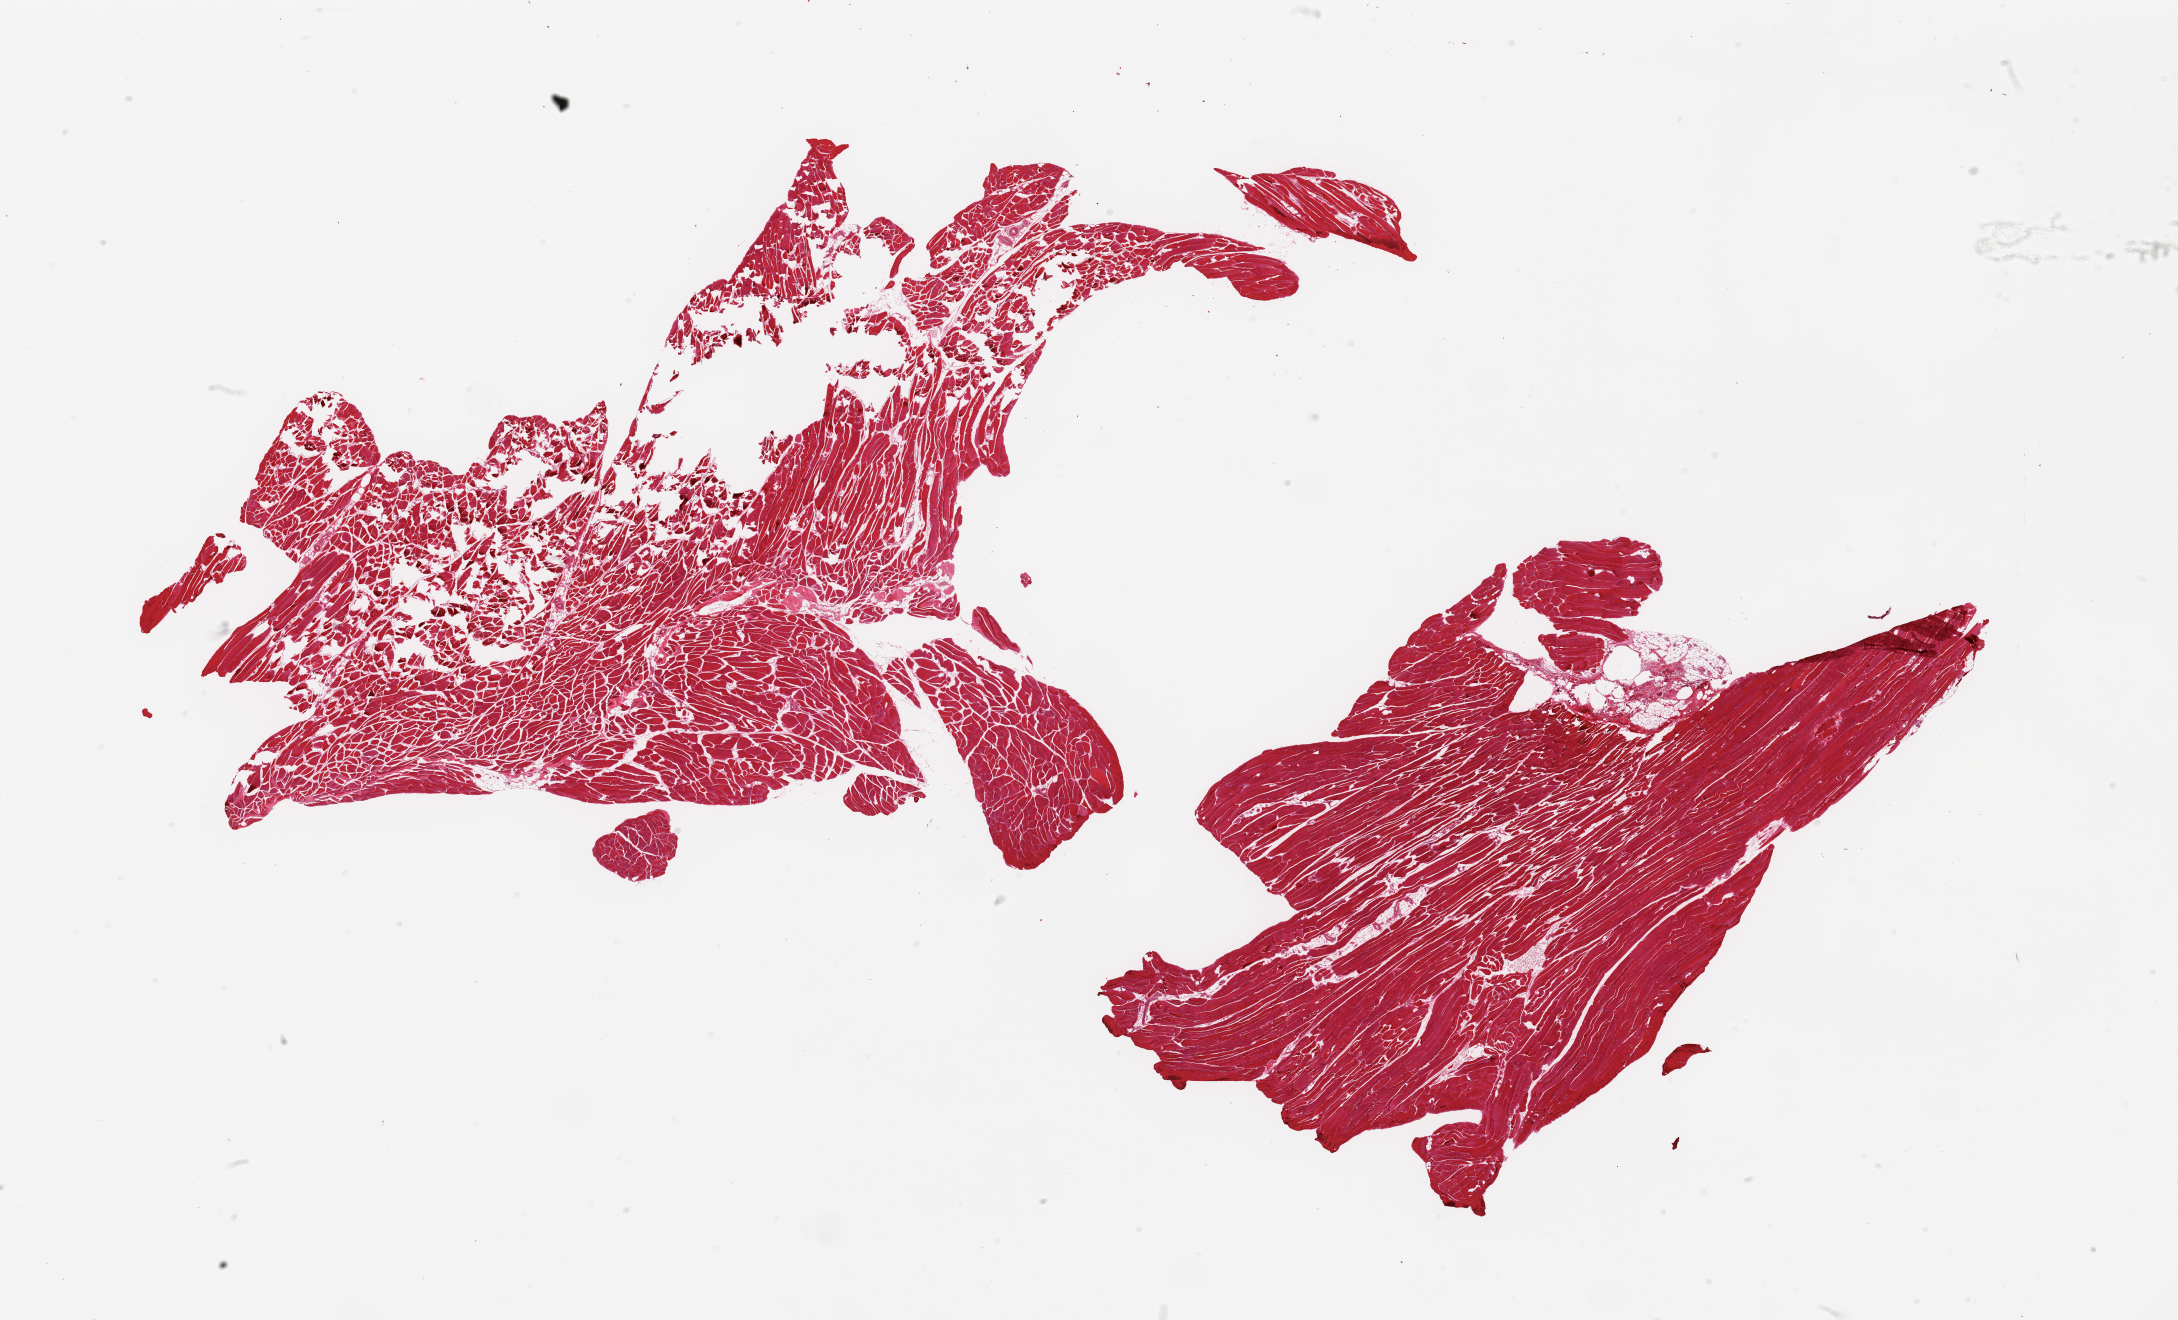
Haematoxylin and eosin whole-slide image, brightfield, shown as a low-resolution overview of the whole scanned area (about 34.5 x 20.9 mm, acquisition: 20x scan), PAXgene-fixed paraffin-embedded (PFPE) section, section of skeletal muscle (target tissue), tissue donor sample. Male donor.
Pathologist's review note for this sample: 2 pieces, minimal interstitial fat2.